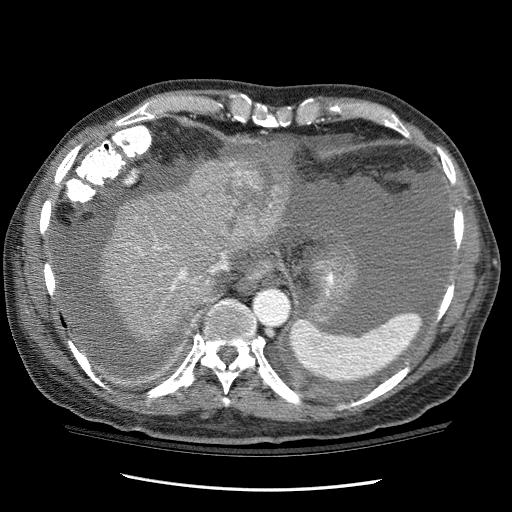
Contrast-enhanced abdominal CT (liver protocol), one axial slice; slice 91 of 114 in the series (ordered by position); one of 3 acquisitions stored at this slice position; soft-tissue window (W 400 / L 40 HU); 512 × 512 image matrix, field of view 360 × 360 mm. From the clinical record (not read from this slice): diagnosis: hepatocellular carcinoma (patient treated with transarterial chemoembolisation; whether this scan precedes or follows treatment is not stated here); TNM stage (as recorded): Stage-I; Child-Pugh class: C; tumour differentiation: well differentiated; tumour nodularity: uninodular.
Outlined on this slice (semi-automatic segmentation, software-assisted and operator-edited):
- liver parenchyma outside the tumour (the mass and vessels are separate outlines, so this box may not span the whole liver): bounding box <100,150,289,338> (left, top, right, bottom; pixels)
- mass: <187,162,287,237>
- liver vessels: <138,246,227,291>